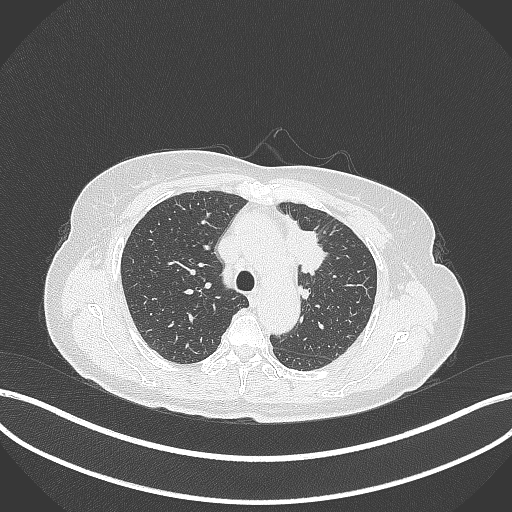
Chest CT, one axial slice; position 240 of 369 along the scan axis; lung window (W 1500 / L -600 HU); 512 × 512 image matrix, field of view 400 × 400 mm. Patient: female, 65 years. From the clinical record (not read from this slice): clinical TNM (as recorded): T2a N0 M0; histopathological grade: G2-3.
Outlined on this slice (bounding box drawn by a radiologist):
- lung tumour (recorded histology: adenocarcinoma): bounding box <281,215,327,276> (left, top, right, bottom; pixels)